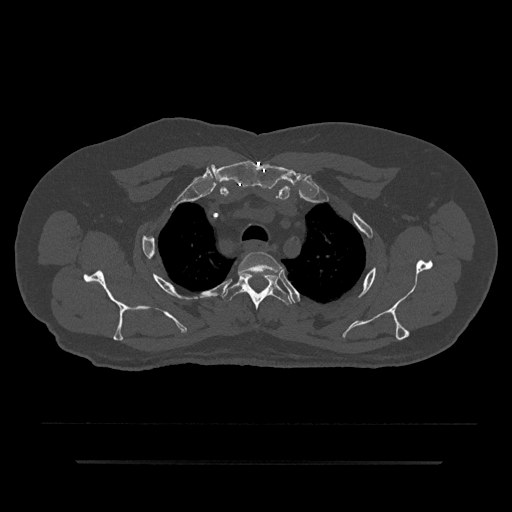
CT including the spine, one axial slice. Position 671 of 797 along the scan axis. Bone window (W 1800 / L 400 HU). 0.5 mm slice thickness. 512 × 512 image matrix, field of view 464 × 464 mm. Patient: male, 59 years. From the clinical record (not read from this slice): primary cancer: bile ducts; vertebrae with lytic lesions (as recorded): T10.
Outlined on this slice (semi-automatic segmentation, software-assisted and operator-edited):
- T2 vertebra: box from (x=238, y=252) to (x=282, y=274) px
- T3 vertebra: (x=223, y=272)–(x=292, y=311)